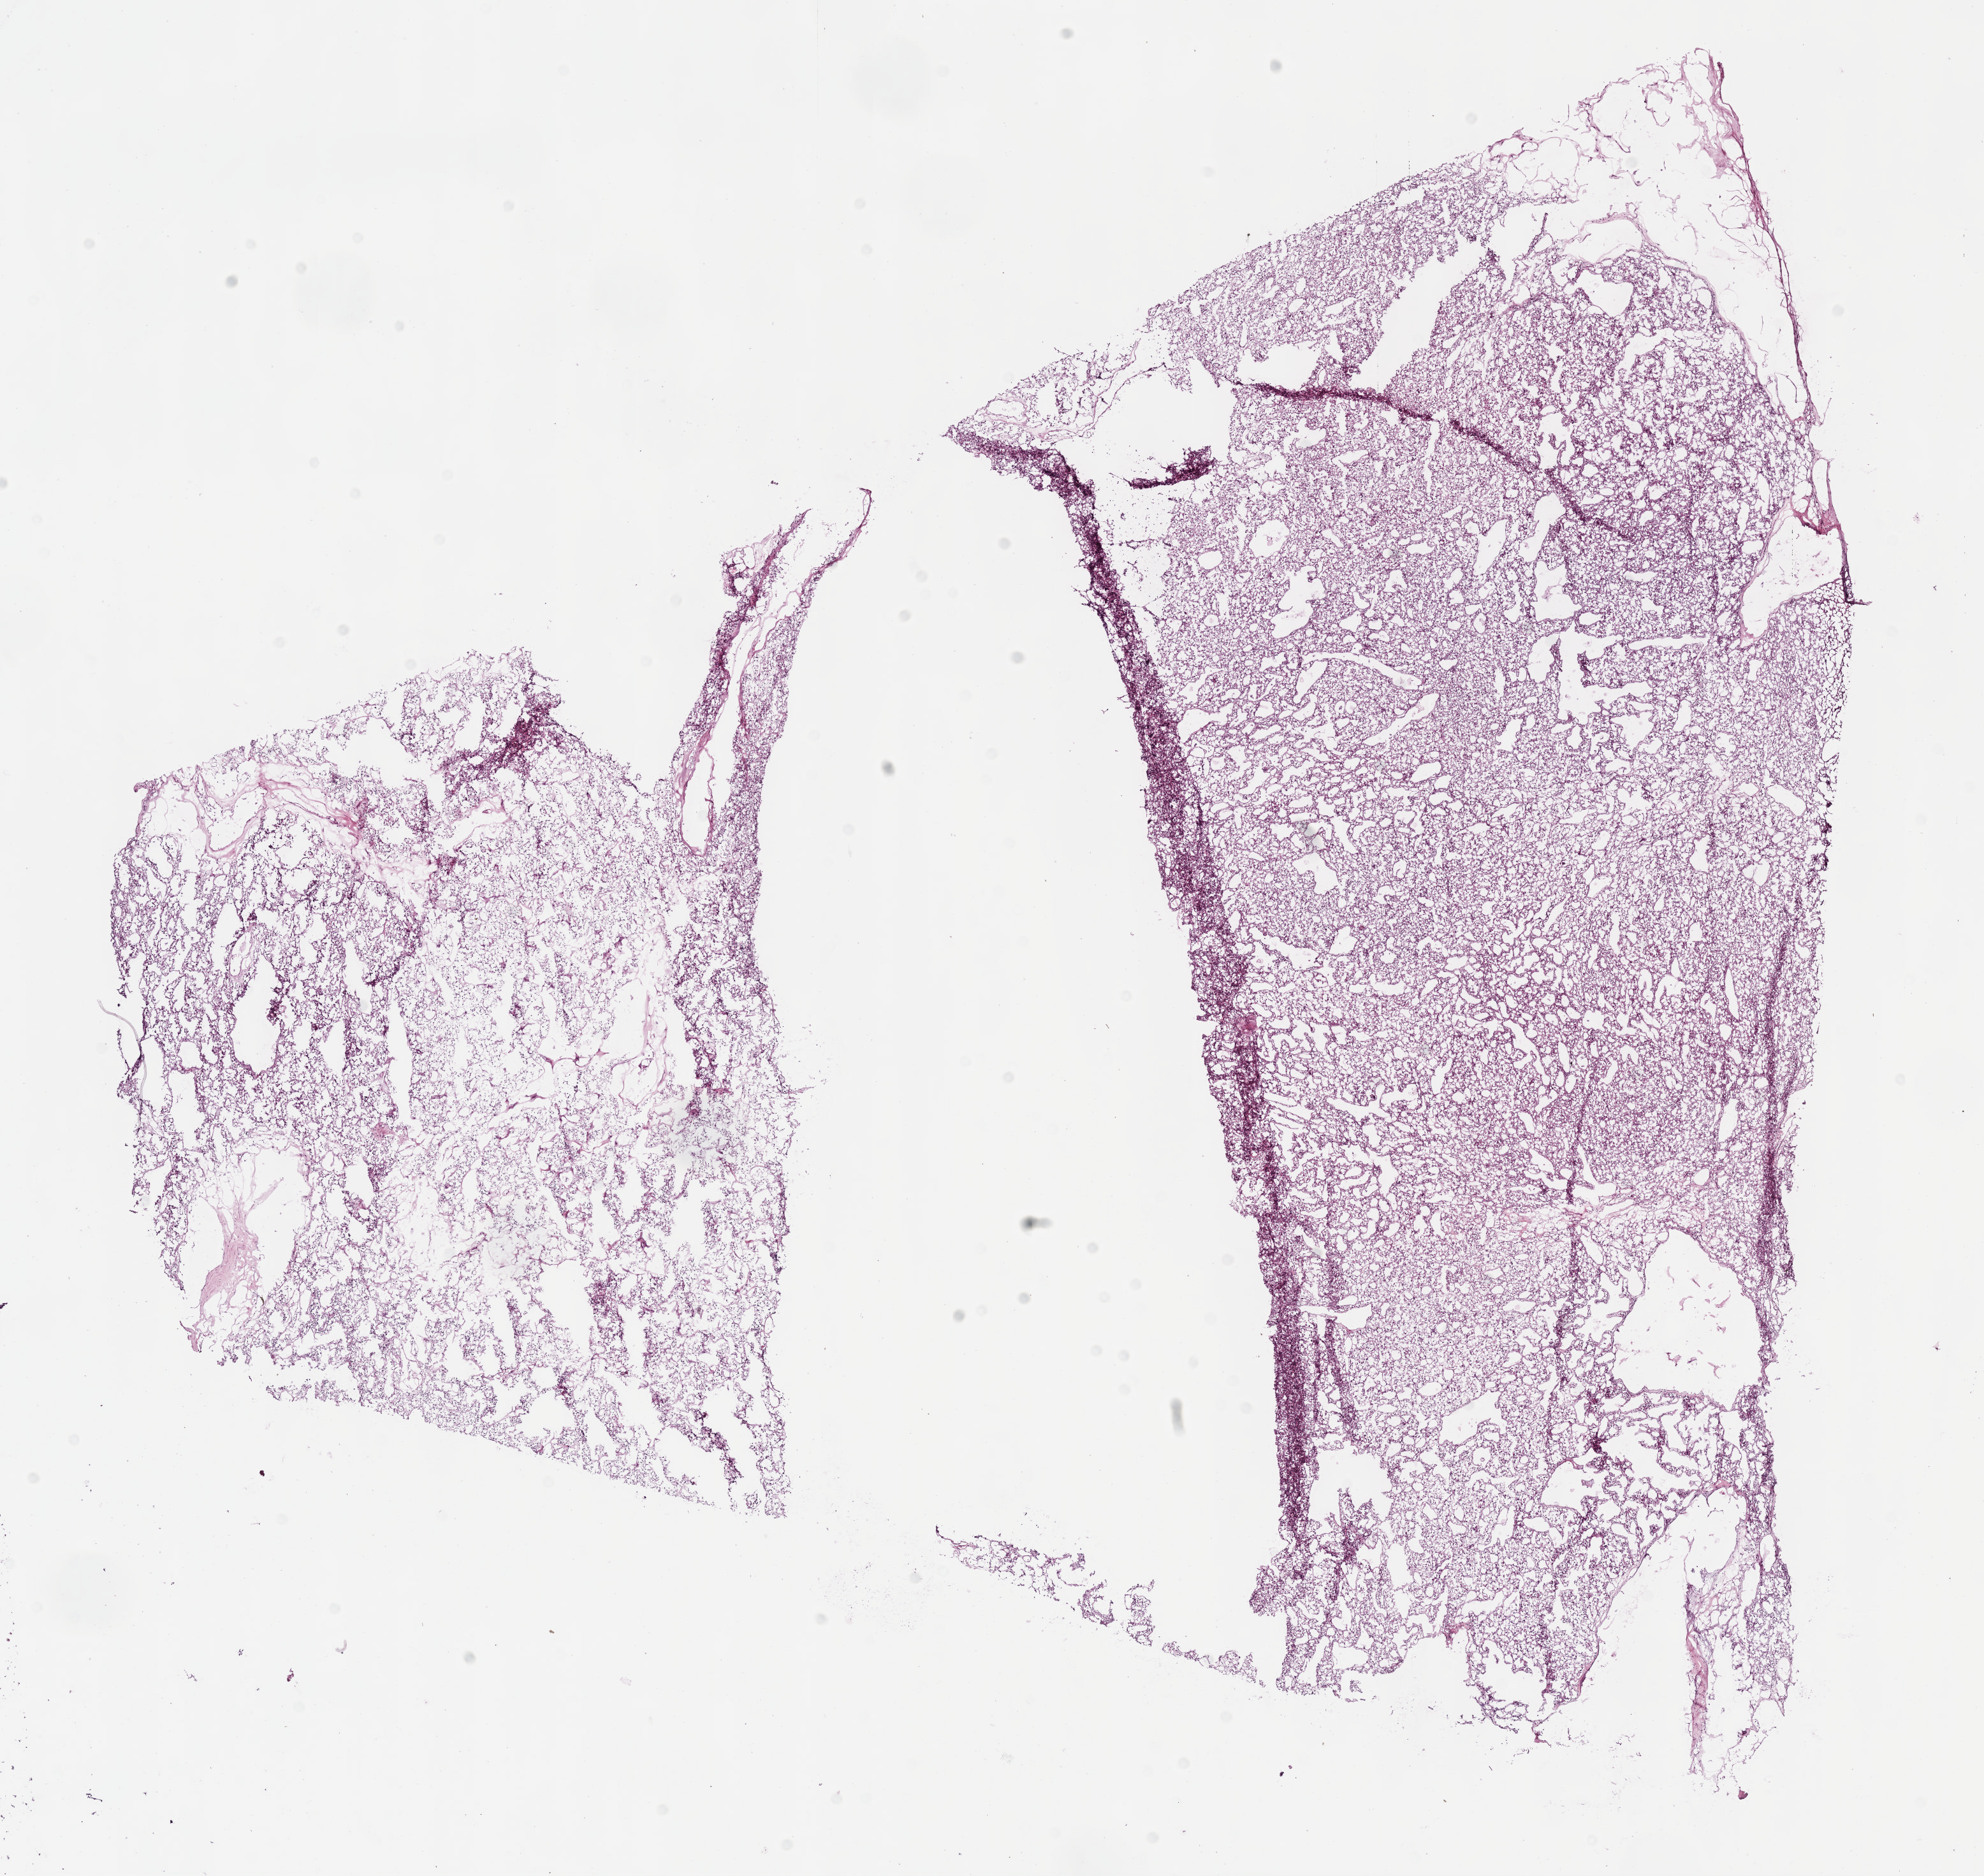
Digitized H&E tissue section (whole slide) — low-resolution overview of the scanned area, about 12.6 x 11.9 mm (from a 40x scan), frozen section, kidney, primary tumour sample. Male patient; age at initial diagnosis 57 years. Histologic grade: G2 (moderately differentiated). Pathologist review of this section (percent, as recorded): tumour cells 95%, tumour nuclei 85%, normal cells 0%, stromal cells 5%, necrosis 0%.
Histologic diagnosis: Clear cell adenocarcinoma, NOS. AJCC pathologic stage: III (7th edition). TNM: T3a NX M0.